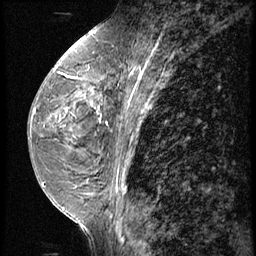
Breast MRI (dynamic contrast-enhanced), one sagittal slice; position 27 of 62 along the scan axis; 3 images stored at this slice position (order not interpretable as contrast timing); 1.5 T; TE 4.2 ms, TR 9 ms; 2.5 mm slice thickness; 256 × 256 image matrix, field of view 180 × 180 mm. Patient: female, 44 years. From the clinical record (not read from this slice): setting: breast cancer imaged before/during neoadjuvant chemotherapy; receptor status: triple-negative.
Annotated regions visible in this slice (semi-automatically segmented with operator editing):
- analysis volume of interest (the breast-tissue region the enhancement analysis was run in; not a lesion): bounding box [x1, y1, x2, y2] px = [67, 64, 116, 125]
- tumour enhancement mask (voxels above the 140 % enhancement threshold inside the analysis volume of interest): [72, 77, 109, 125]